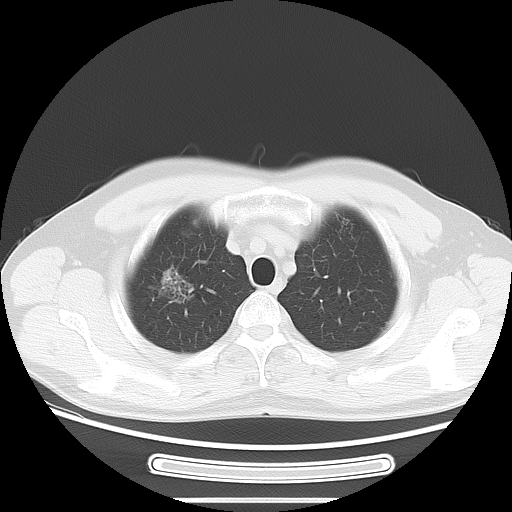
Chest CT, one axial slice. Position 56 of 68 along the scan axis. Reconstruction kernel LUNG. Lung window (W 1500 / L -600 HU). 5 mm slice thickness. 512 × 512 image matrix. Patient: male, 53 years. From the clinical record (not read from this slice): clinical TNM (as recorded): T1c N0 M0.
Annotated regions visible in this slice (rectangle marked by the reading radiologist):
- lung tumour (recorded histology: adenocarcinoma): bounding box <147,260,201,312> (left, top, right, bottom; pixels)